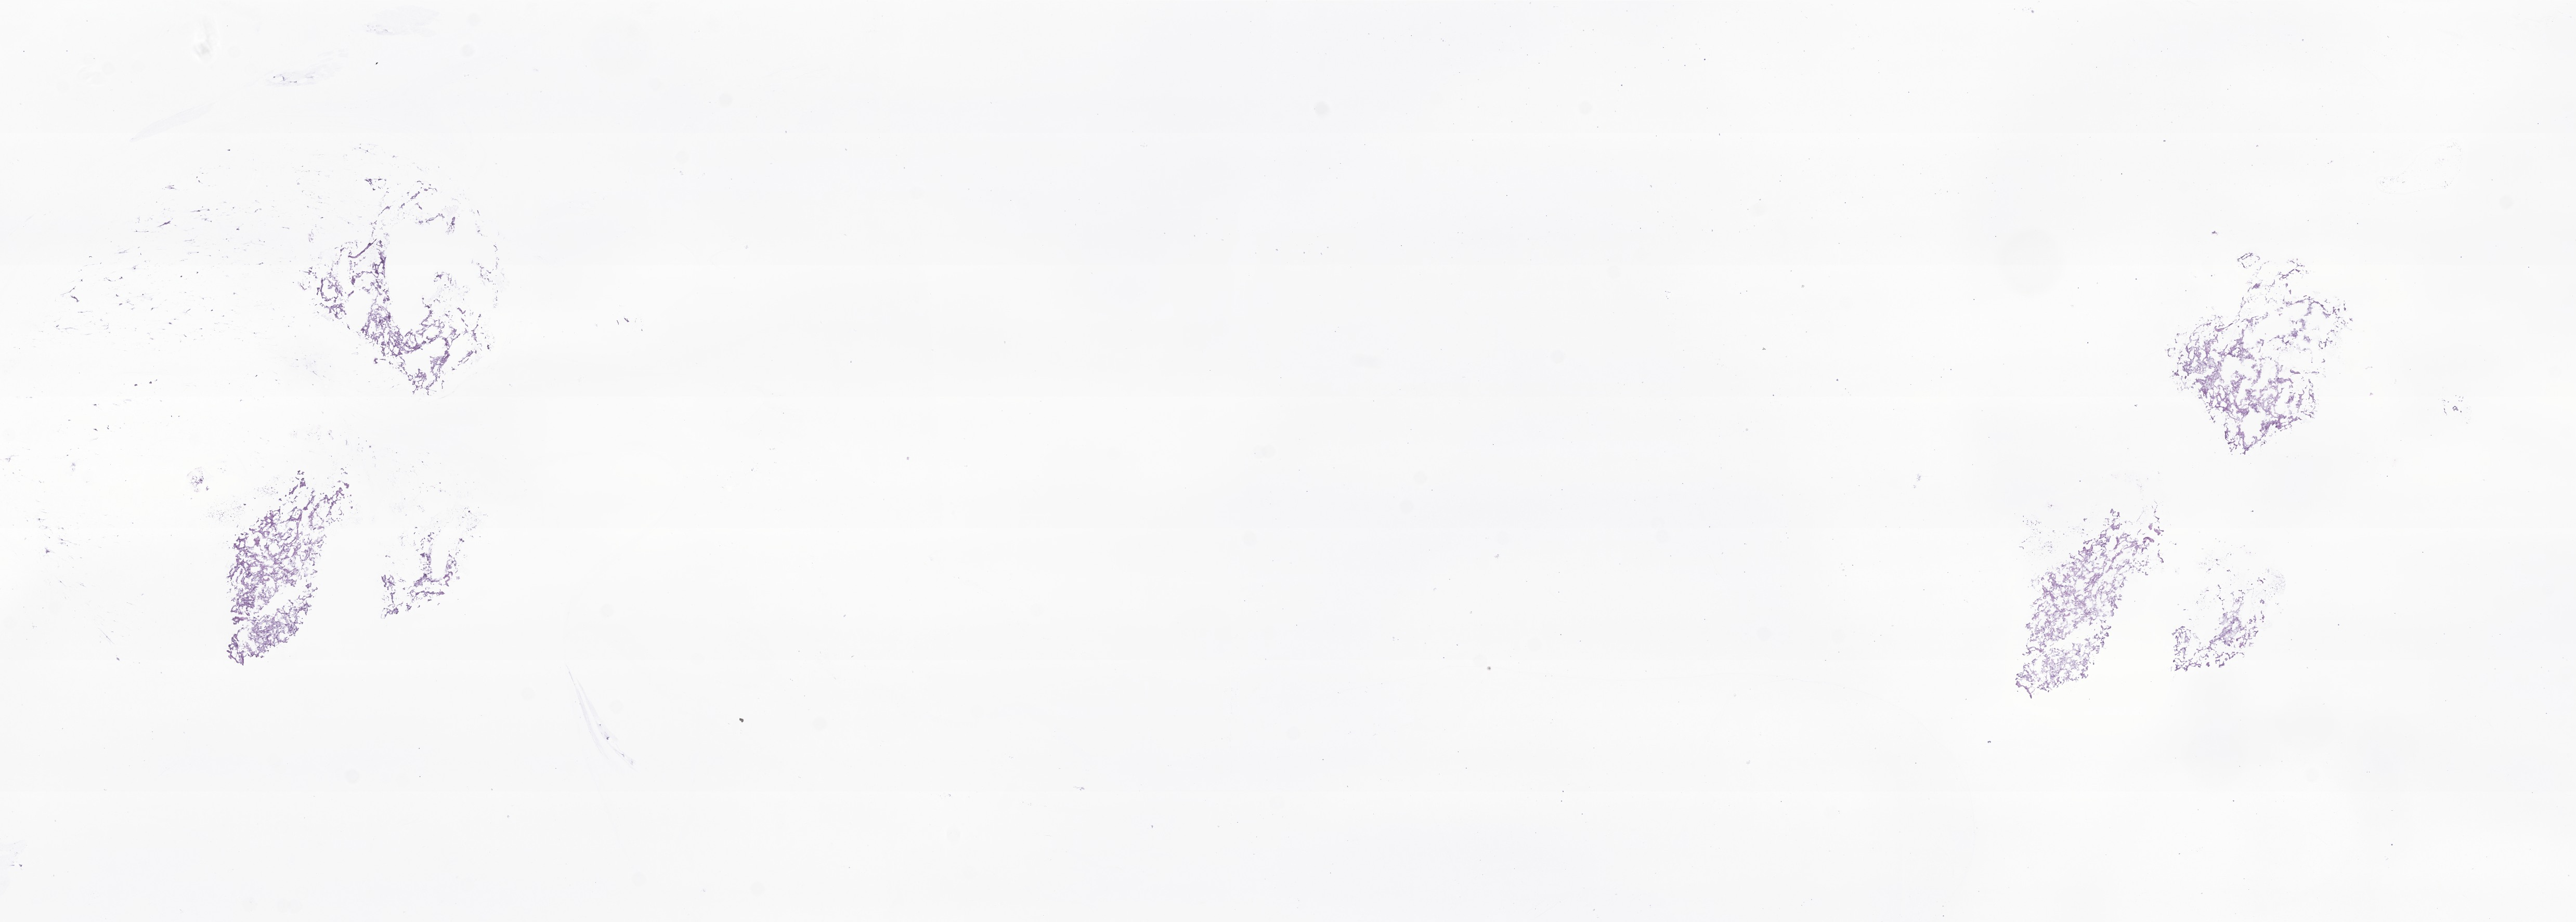
Hematoxylin and eosin (H&E) whole-slide image of tumor tissue from the brain, low-resolution overview of the scanned area, about 20.9 x 7.5 mm; cryosection (OCT / tissue freezing medium). Female patient, age 112 months (9 years 4 months).
• diagnosis (ICD-O-3 morphology term): Ganglioglioma, NOS